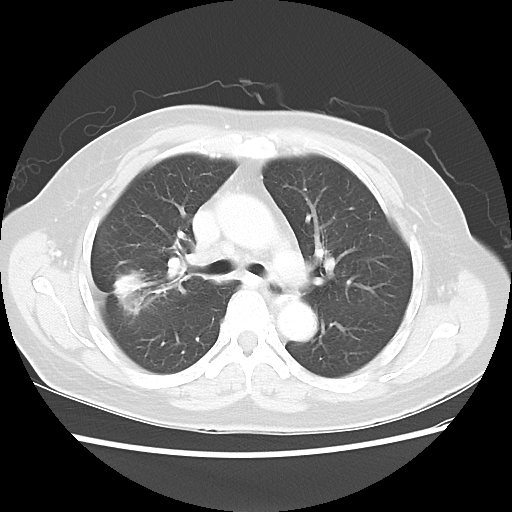
Chest CT, one axial slice. Position 22 of 40 along the scan axis. Reconstruction kernel LUNG. 100 kVp. Lung window (W 1500 / L -600 HU). 512 × 512 image matrix. Patient: female, 67 years. Case-level facts recorded for this patient, not image findings: clinical TNM (as recorded): T1c N1 M0.
Structures marked on this image (rectangle marked by the reading radiologist):
- lung tumour (recorded histology: adenocarcinoma): bounding box <107,262,155,324> (left, top, right, bottom; pixels)